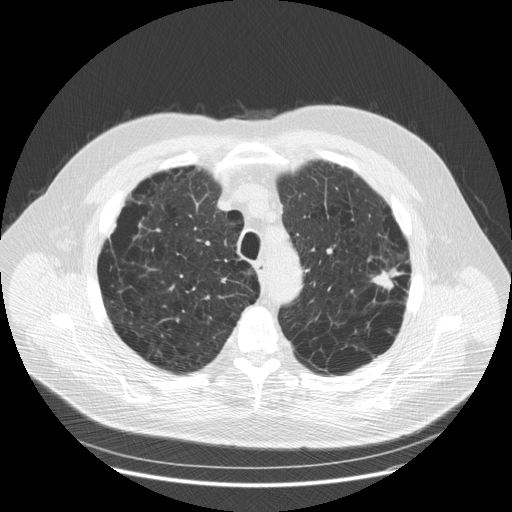
Chest CT (low-dose screening protocol), one axial image, baseline annual screen, lung window (W 1500 / L -600 HU), 120 kVp, slice 42 of 179 in the series. Male participant, aged 70 years at enrolment. Current smoker at enrolment.
Expert reader's lesion annotation, bounding box <363,250,416,300> (left, top, right, bottom; pixels). Screening reader's record for this exam (one nodule recorded; not confirmed to be the boxed lesion): non-calcified nodule or mass ≥4 mm, left upper lobe, 25 × 13 mm, spiculated (stellate) margins, soft tissue attenuation.